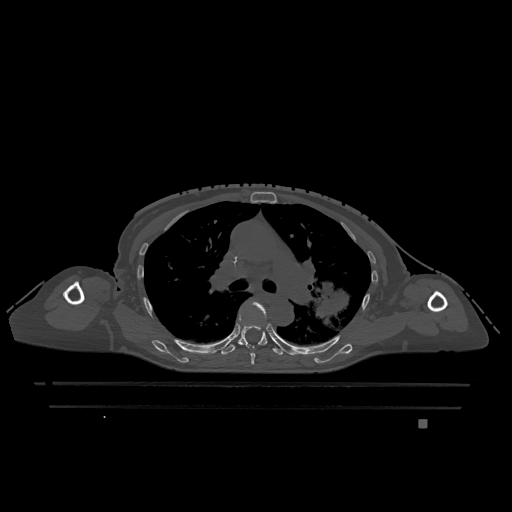
CT including the spine, one axial slice; slice 809 of 1317 in the series (ordered by position); bone window (W 1800 / L 400 HU); 512 × 512 image matrix, field of view 500 × 500 mm. Patient: female, 74 years. Case-level facts recorded for this patient, not image findings: primary cancer: lung.
Structures marked on this image (semi-automatically segmented with operator editing):
- T5 vertebra: bounding box <250,302,266,365> (left, top, right, bottom; pixels)
- T6 vertebra: <221,308,283,355>